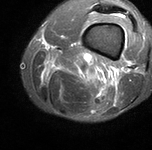
MRI of an extremity soft-tissue mass, one axial slice; position 18 of 90 along the scan axis; STIR; MR volume resampled by the dataset authors to the PET/CT grid (not the native acquisition matrix); 3.27 mm slice thickness; 152 × 150 image matrix, field of view 148 × 146 mm. Male patient. Case-level facts recorded for this patient, not image findings: histological type: undifferentiated pleomorphic liposarcoma; grade: high; site of the primary tumour: left thigh.
Structures marked on this image (expert contour drawn on MRI and transferred to this co-registered scan by the dataset authors):
- gross tumour volume including surrounding oedema: bounding box <45,60,60,81> (left, top, right, bottom; pixels)